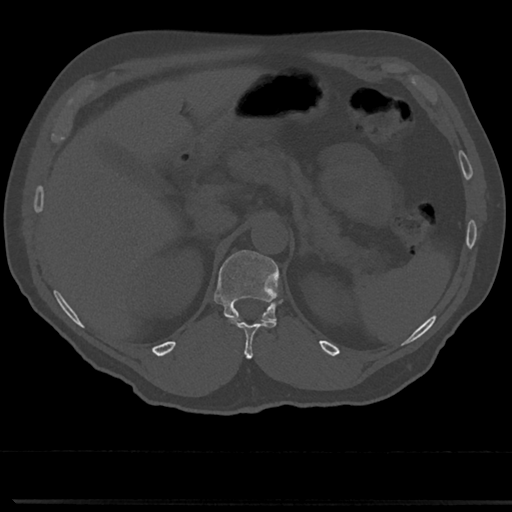
CT including the spine, one axial slice; slice 170 of 817 in the series (ordered by position); reconstruction kernel Br40s/3; bone window (W 1800 / L 400 HU); 512 × 512 image matrix. Male patient, age 61 years. From the clinical record (not read from this slice): primary cancer: prostate.
Annotated regions visible in this slice (semi-automatically segmented with operator editing):
- T11 vertebra: box from (x=243, y=325) to (x=253, y=358) px
- T12 vertebra: (x=214, y=250)–(x=286, y=337)